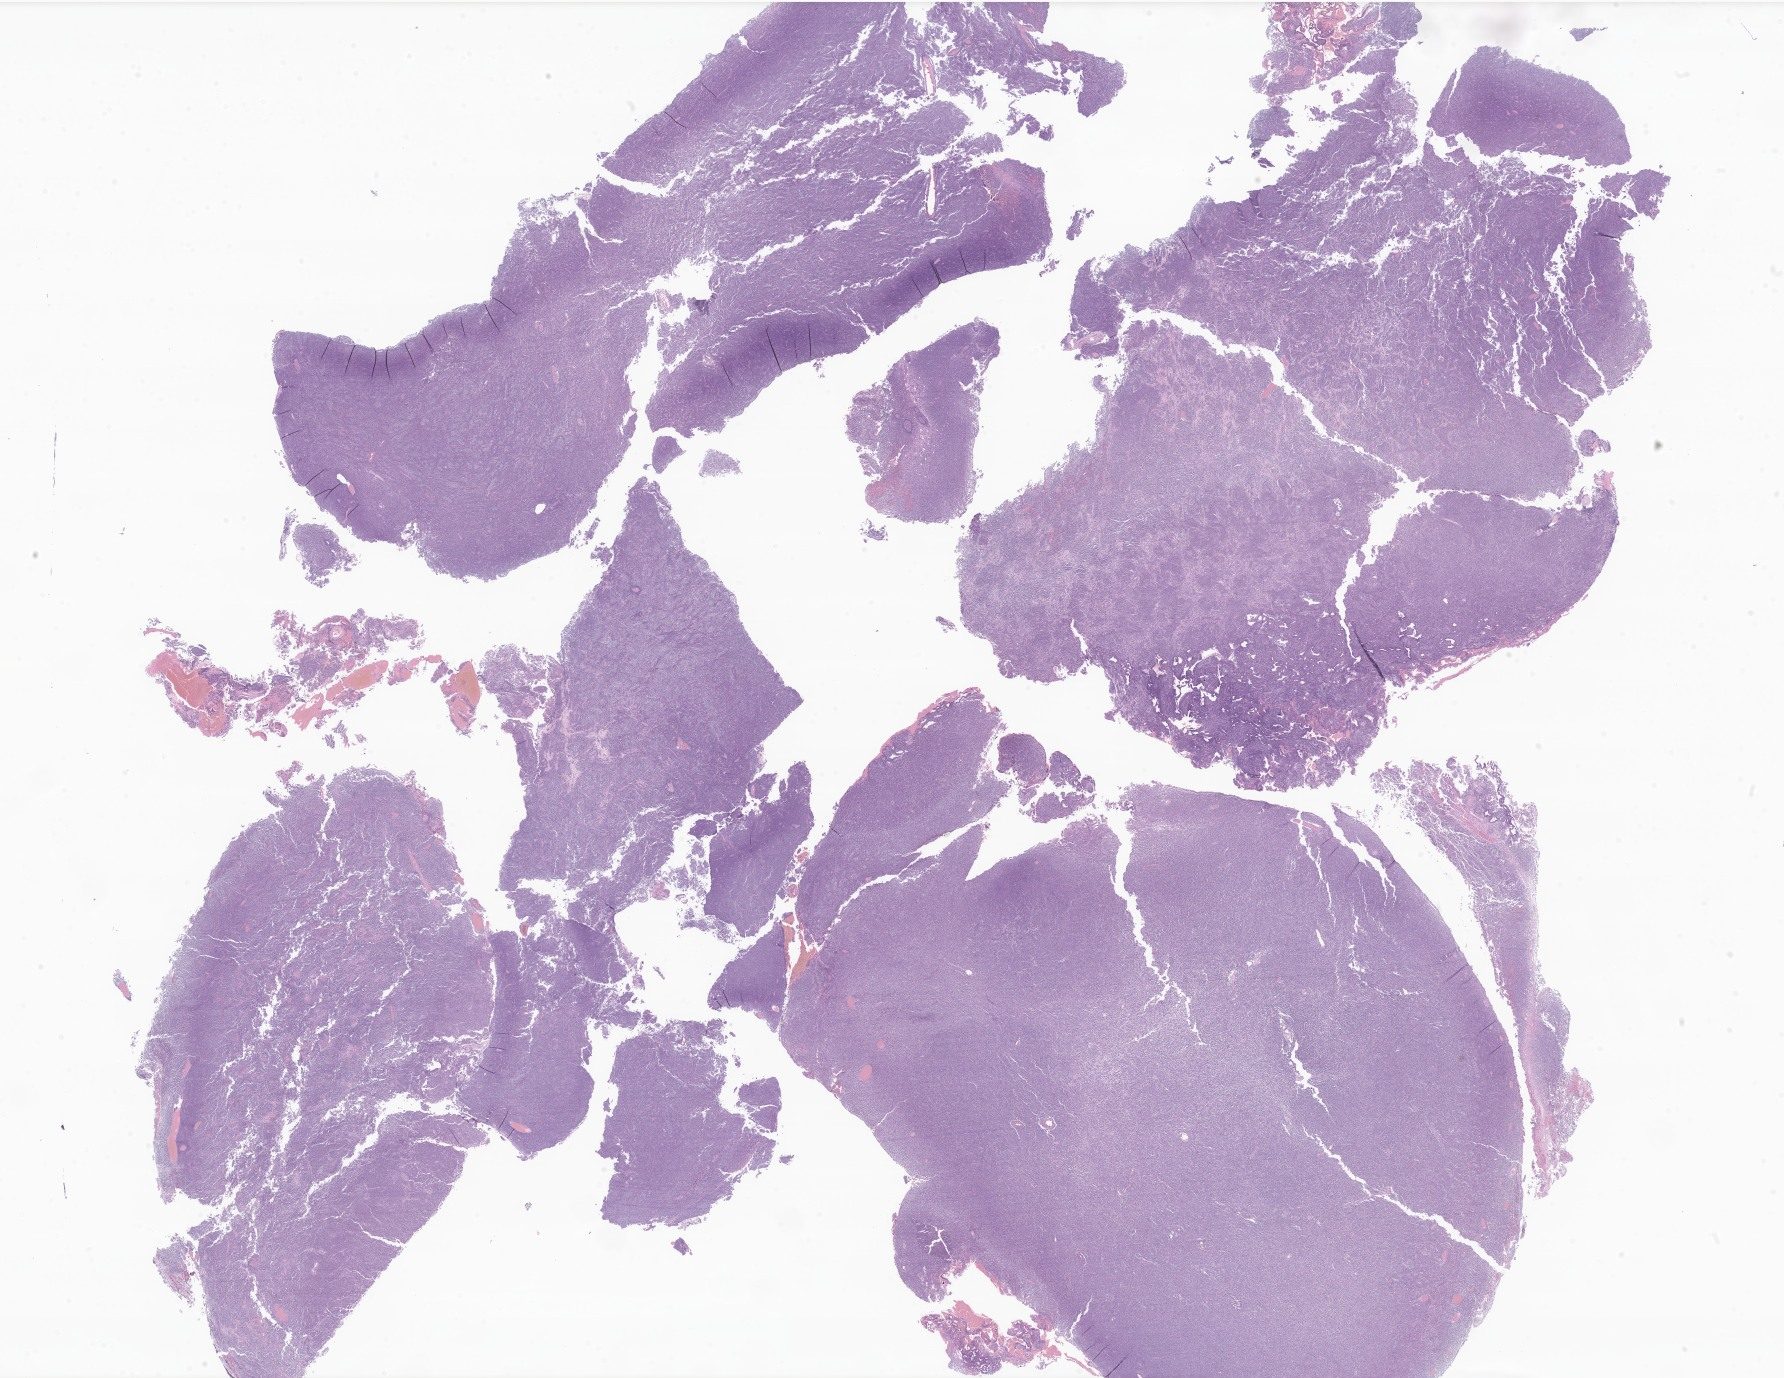
Digitized H&E-stained section of tumor tissue from the central nervous system — shown as a low-resolution overview of the whole scanned area (about 30.1 x 23.2 mm); FFPE section. Patient: male.
Recorded diagnosis: Embryonal tumor with histomorphologic features suggestive of med.